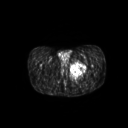
FDG PET of an extremity soft-tissue mass (from a PET/CT study), one axial slice. Slice 39 of 267 in the series (ordered by position). 3.27 mm slice thickness. 128 × 128 image matrix, field of view 600 × 600 mm. Male patient, age 59 years. Case-level facts recorded for this patient, not image findings: histological type: pleiomorphic liposarcoma; grade: high; site of the primary tumour: left thigh.
Outlined on this slice (expert contour drawn on MRI and transferred to this co-registered scan by the dataset authors):
- gross tumour volume including surrounding oedema: bounding box [x1, y1, x2, y2] px = [70, 61, 86, 79]
- gross tumour volume (mass): [70, 62, 85, 76]